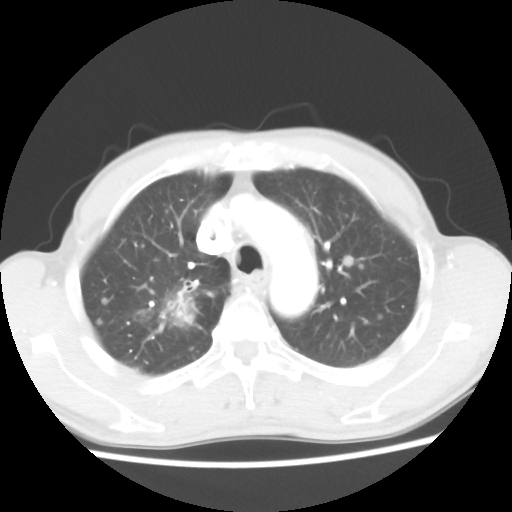
Chest CT, one axial slice. Reconstruction kernel STANDARD. Lung window (W 1500 / L -600 HU). 512 × 512 image matrix. Patient: male, 66 years. From the clinical record (not read from this slice): clinical TNM (as recorded): T2 N0 M1a.
Structures marked on this image (bounding box drawn by a radiologist):
- lung tumour (recorded histology: adenocarcinoma): box from (x=137, y=275) to (x=219, y=343) px